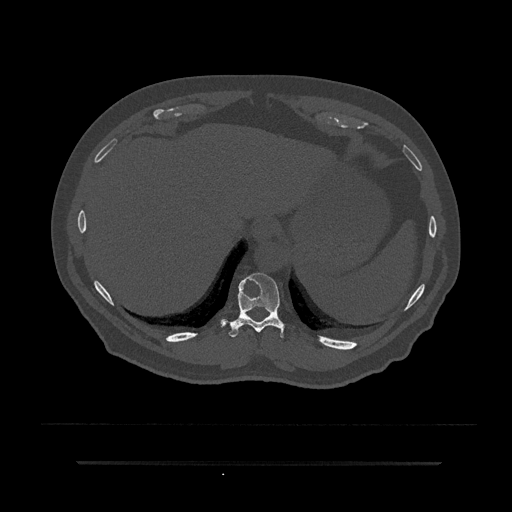
CT including the spine, one axial slice; position 326 of 797 along the scan axis; 120 kVp; bone window (W 1800 / L 400 HU); 0.5 mm slice thickness; 512 × 512 image matrix, field of view 464 × 464 mm. Male patient, age 59 years. Case-level facts recorded for this patient, not image findings: primary cancer: bile ducts; vertebrae with lytic lesions (as recorded): T10.
Structures marked on this image (semi-automatic segmentation, software-assisted and operator-edited):
- T10 vertebra: bounding box (x1, y1, x2, y2) in pixels: (221, 273, 285, 338)